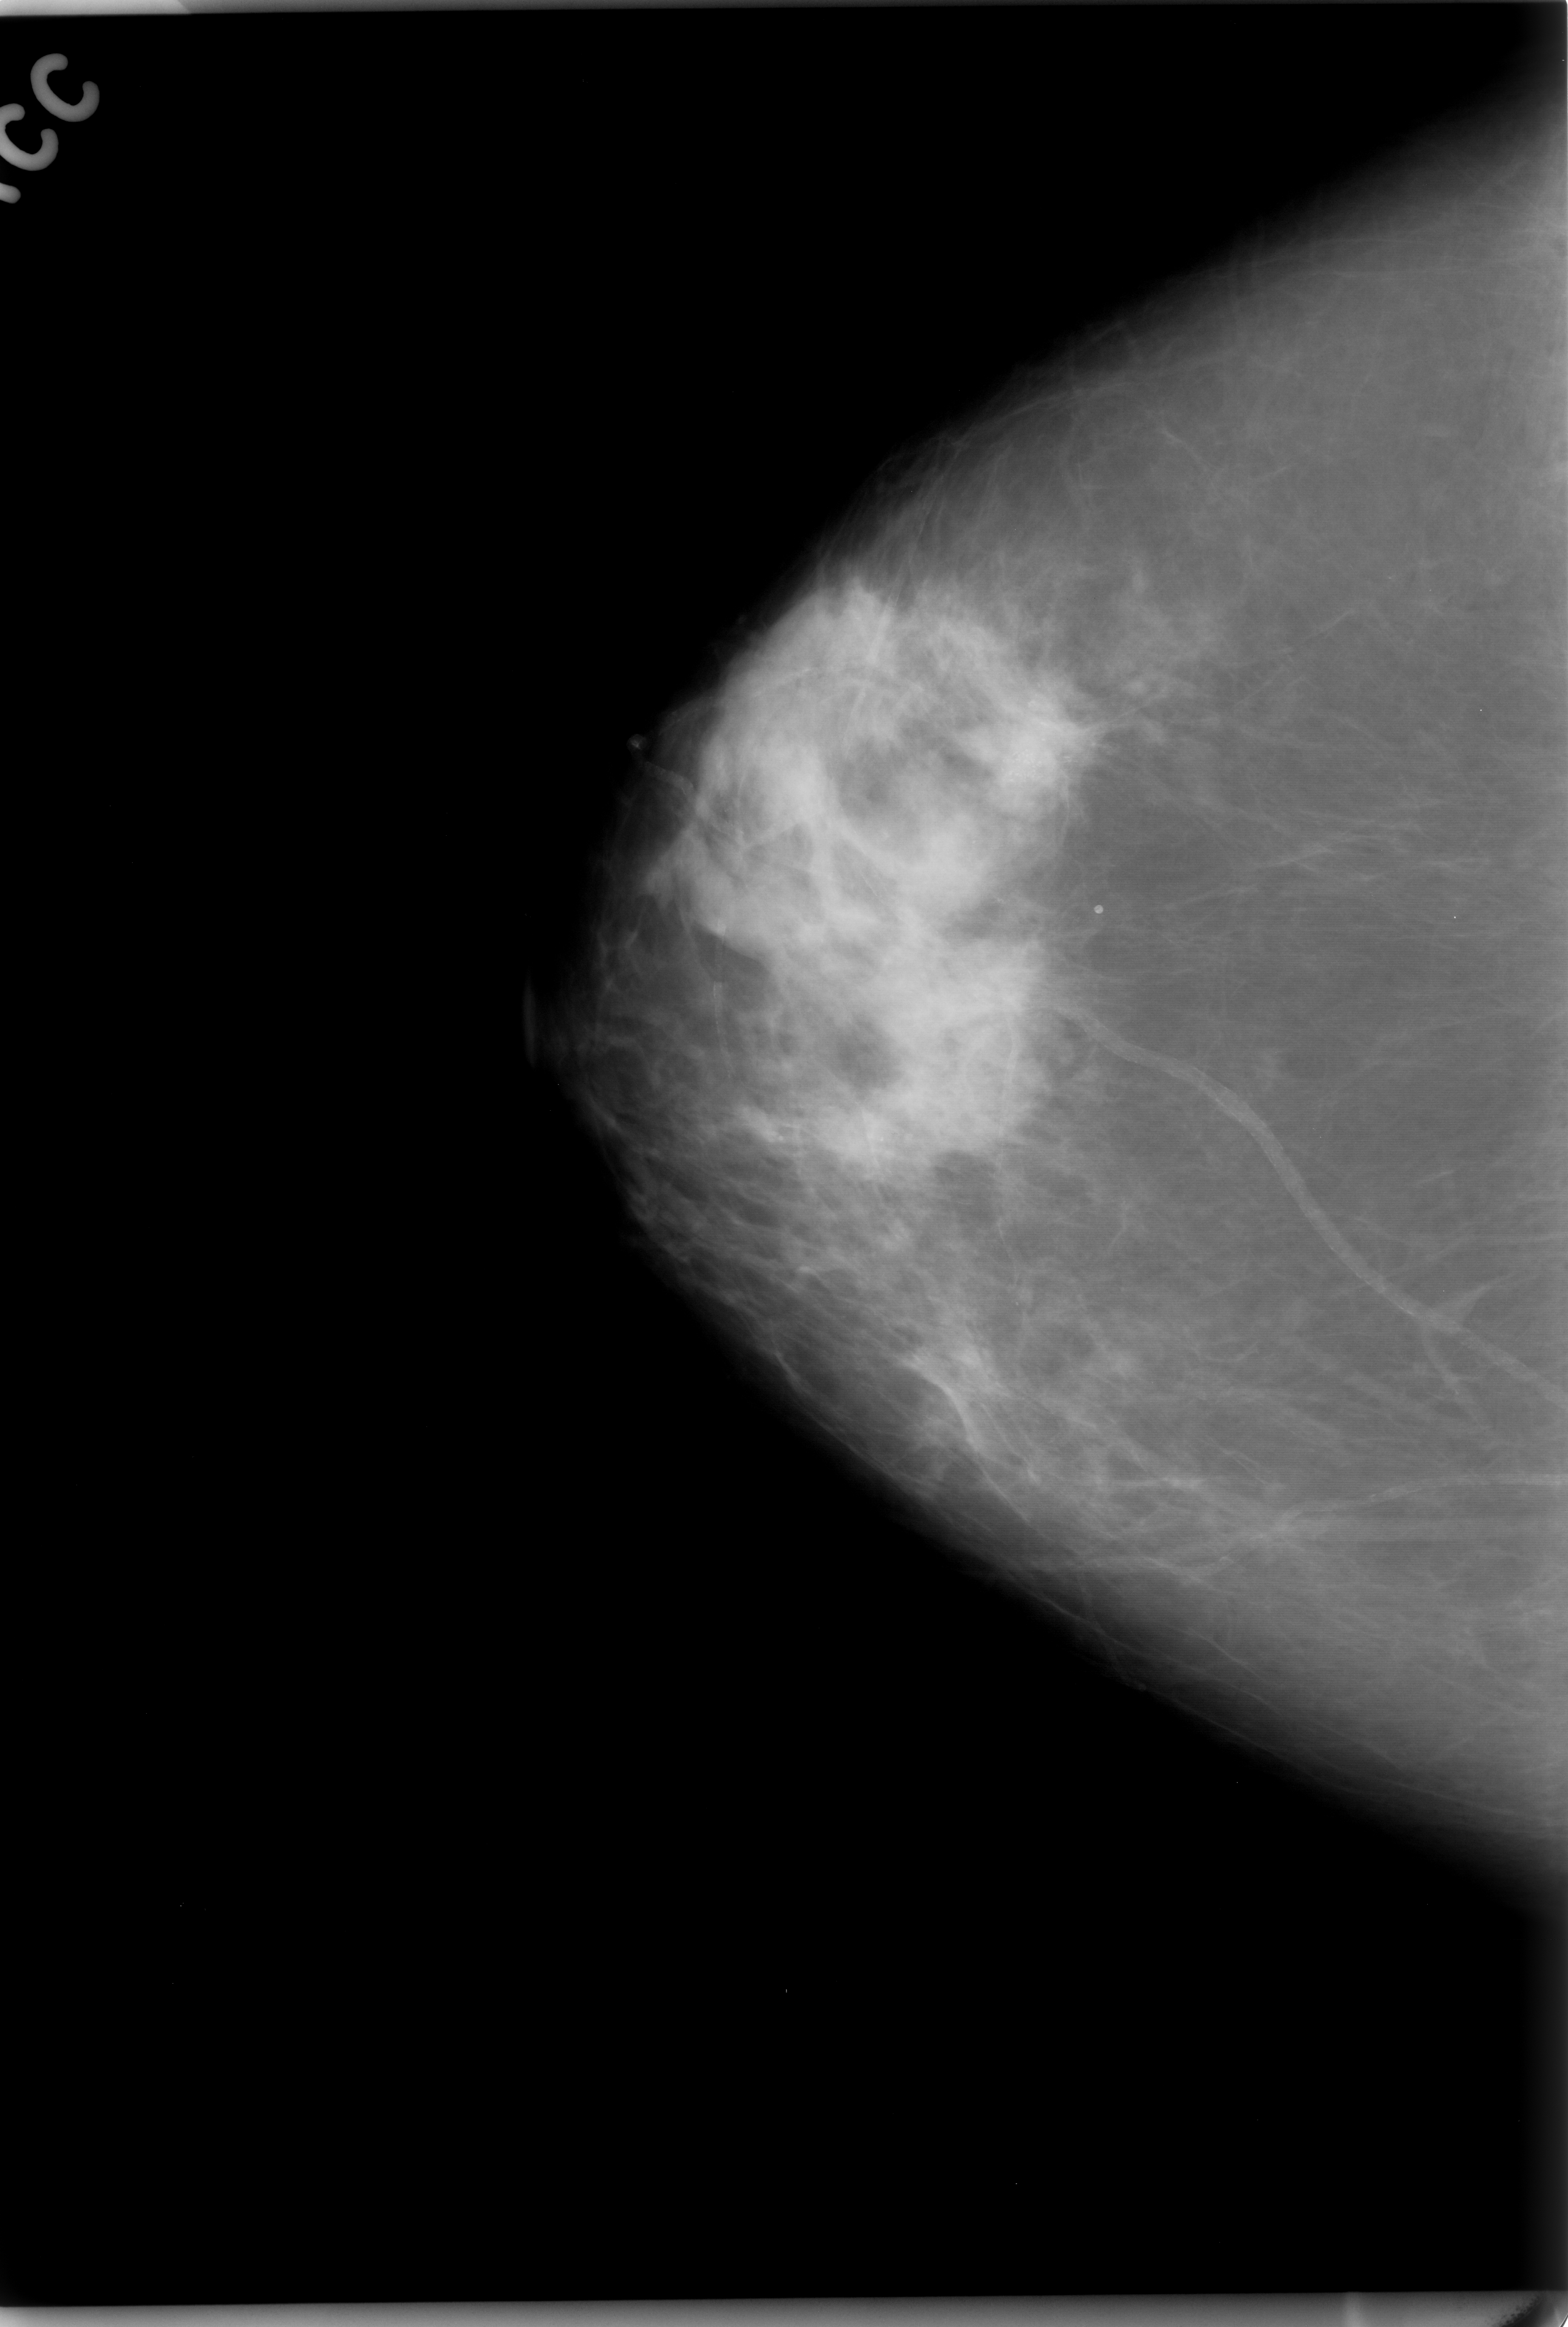
Scanned film-screen mammogram. Right breast. Craniocaudal (CC) view. Breast composition: scattered fibroglandular densities (BI-RADS density category 2 of 4). 1568 × 2327 image matrix.
Expert-marked regions of interest on this film, with their recorded descriptors:
- calcifications, morphology pleomorphic, distribution clustered; BI-RADS assessment category 5; subtlety rating 4 on a 1 (subtle) to 5 (obvious) scale; pathology (as recorded): malignant: bounding box <964,628,1144,852> (left, top, right, bottom; pixels)